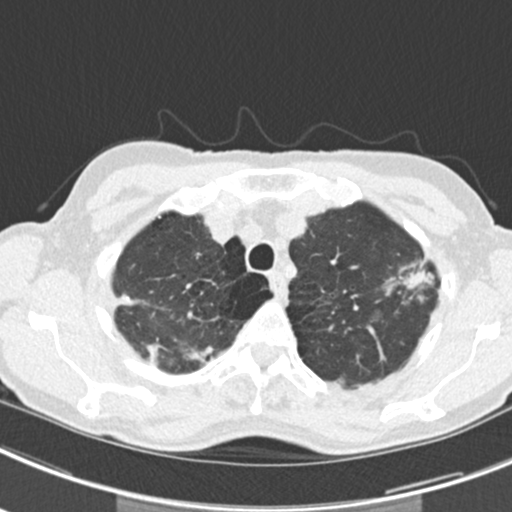
Low-dose screening chest CT, axial slice; second screening round (one year after baseline); lung window (W 1500 / L -600 HU); 2 mm slice thickness; standard (soft-tissue) reconstruction kernel (B30f); 512 × 512 image matrix. Female, age 63 years at enrolment.
• Lesion marked by an expert reader, bounding box [x1, y1, x2, y2] px = [377, 247, 441, 308].
• The screening reader recorded 9 non-calcified nodules or masses ≥4 mm on this exam (left upper lobe, right upper lobe, left upper lobe, left lower lobe, right middle lobe, left lower lobe, left lower lobe, right lower lobe, right lower lobe); which of them this box marks is not recorded.
• Participant outcome: lung cancer diagnosed 408 days after this screen (after the third annual screen) — bronchiolo-alveolar adenocarcinoma, NOS, right upper lobe, right middle lobe, right lower lobe, left upper lobe, left lower lobe, moderately differentiated (G2), stage IV (AJCC 6th edition).